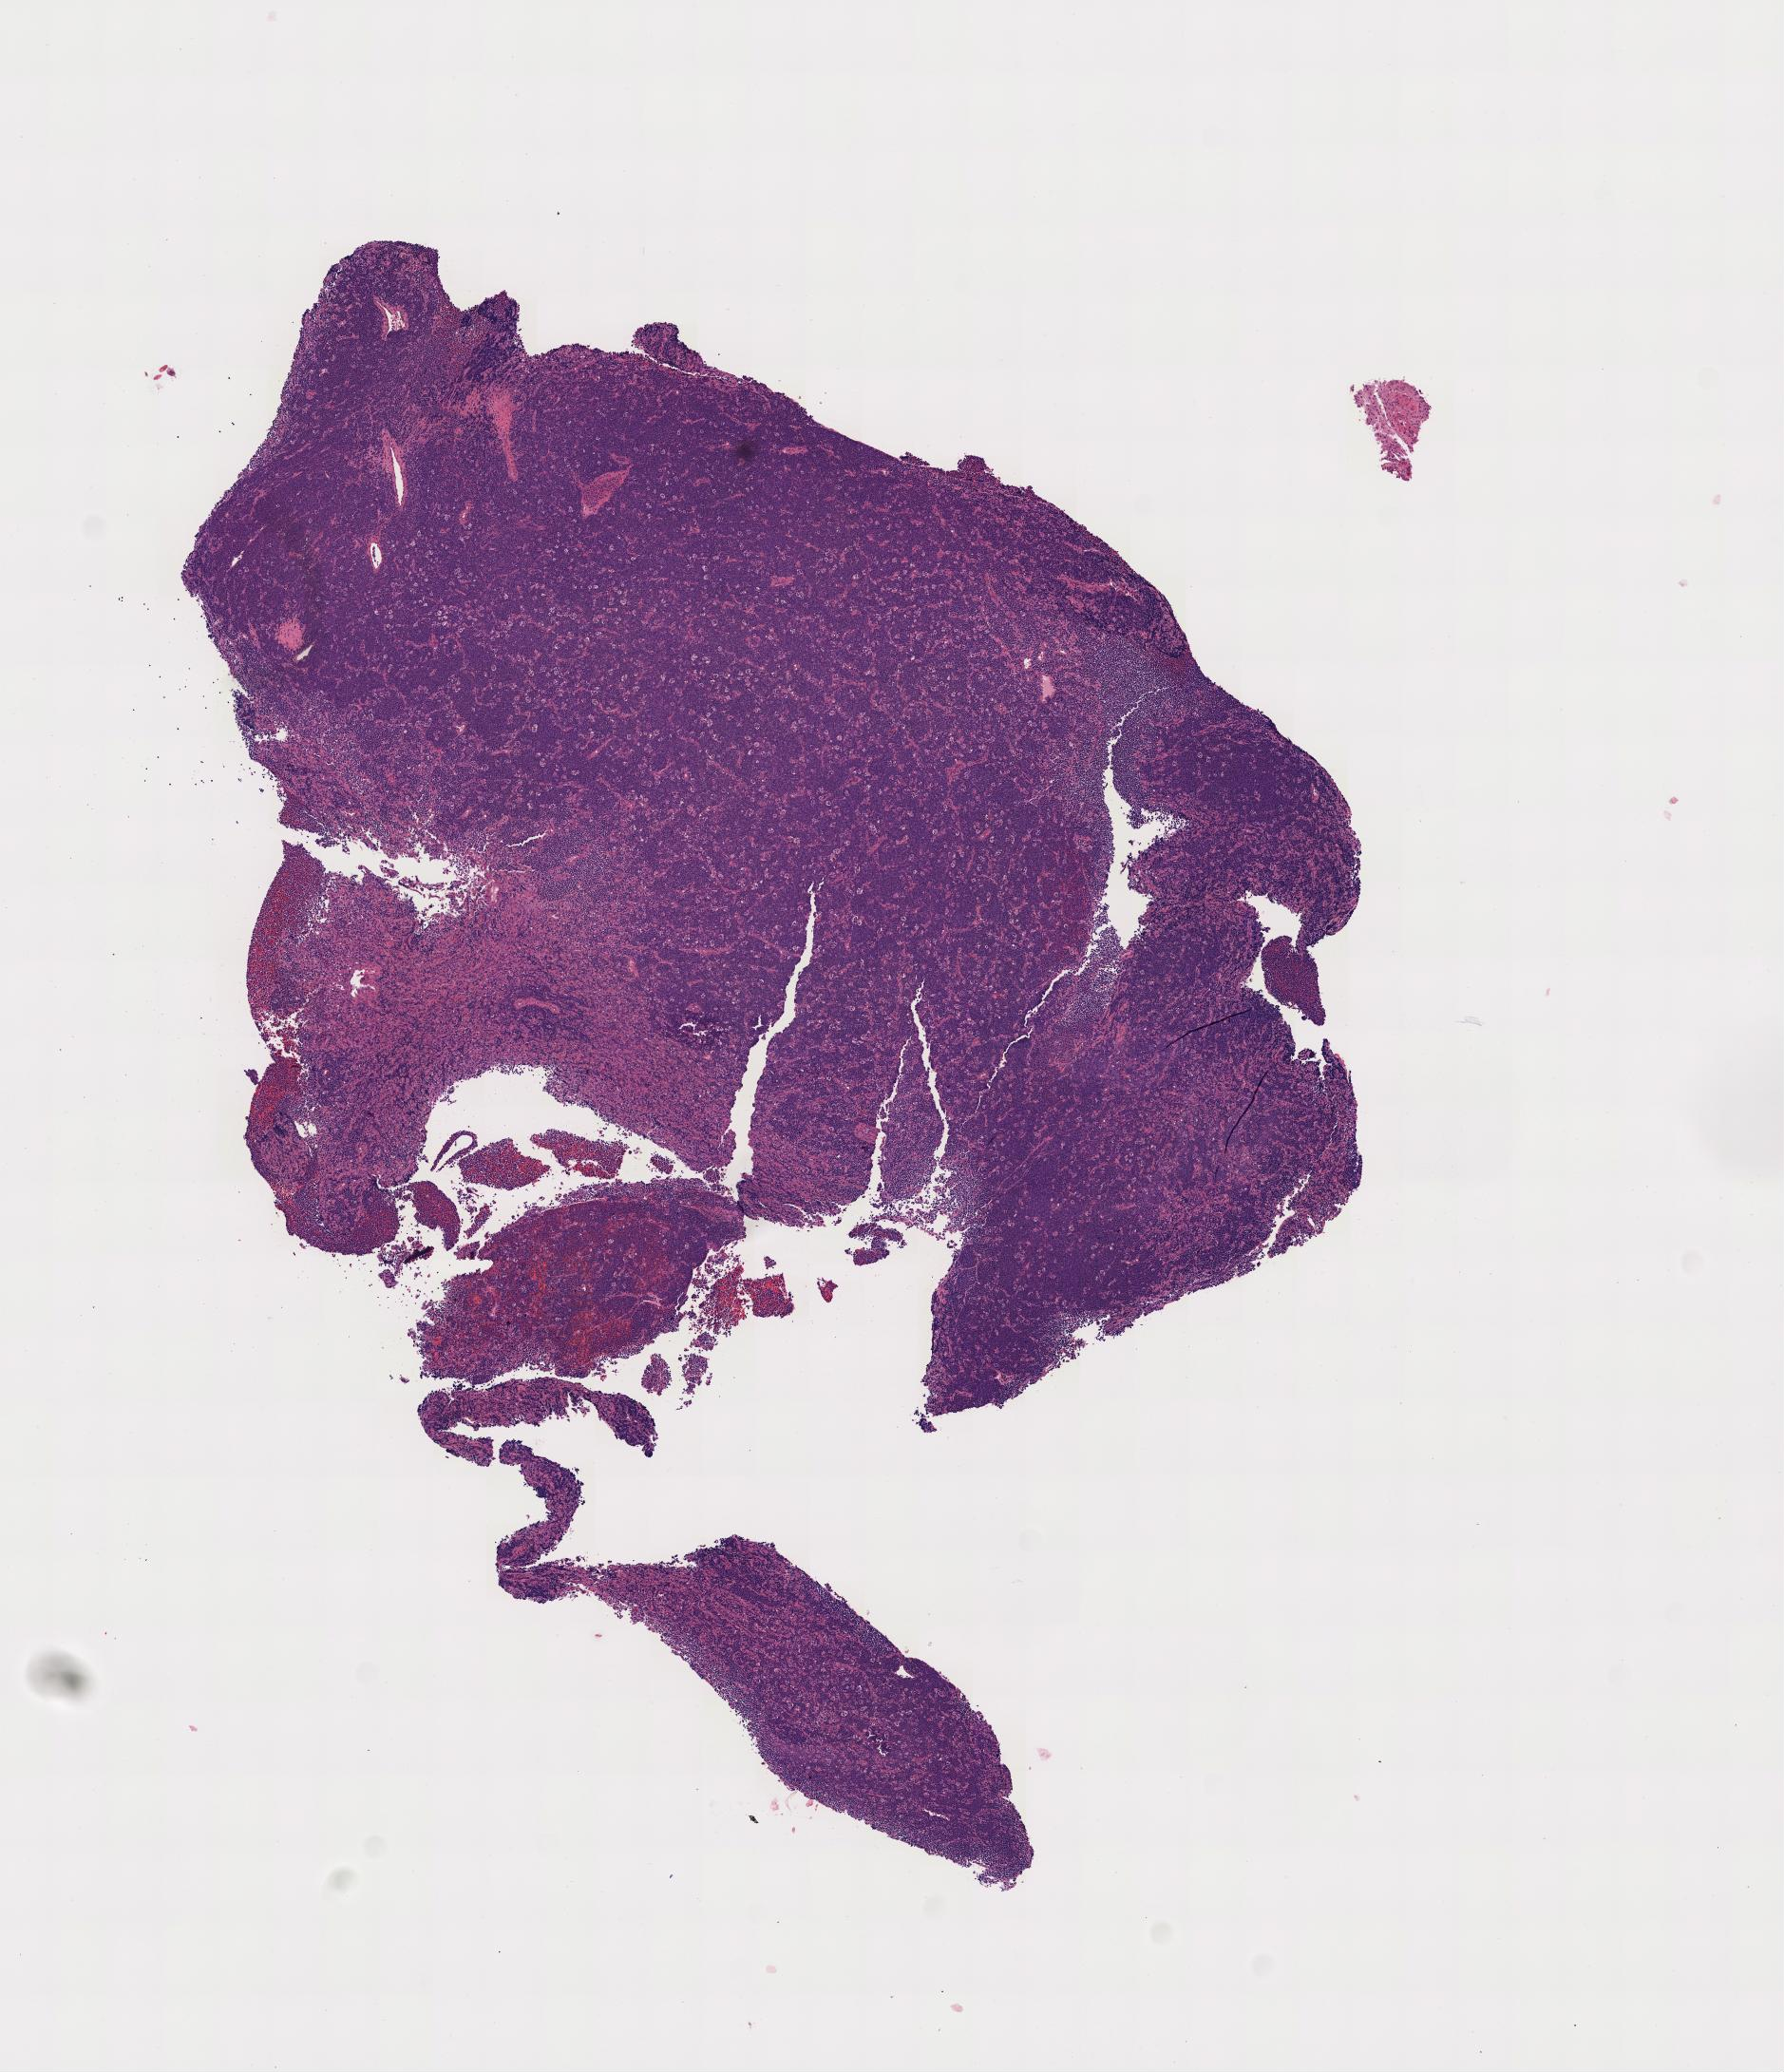
Haematoxylin and eosin whole-slide image, whole scanned area shown as a low-resolution overview, specimen: tumor tissue, anatomic site: cranium. Male, age 6 years at initial diagnosis.
Diagnosis: Burkitt lymphoma, NOS.